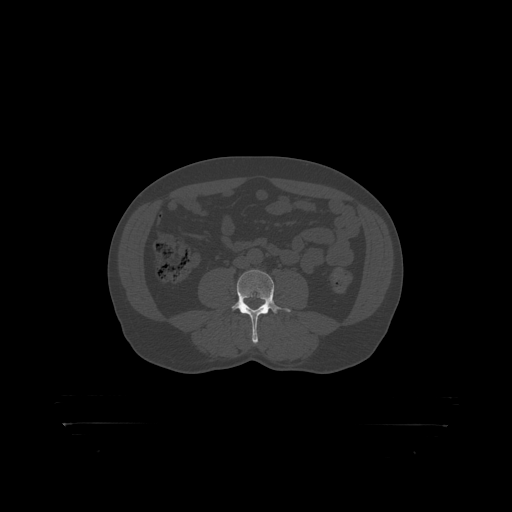
CT including the spine, one axial slice; slice 237 of 399 in the series (ordered by position); reconstruction kernel STANDARD; 120 kVp; bone window (W 1800 / L 400 HU); 1.25 mm slice thickness; 512 × 512 image matrix, field of view 650 × 650 mm. Male patient, age 46 years. From the clinical record (not read from this slice): primary cancer: skin.
Structures marked on this image (semi-automatic segmentation, software-assisted and operator-edited):
- L4 vertebra: bounding box (x1, y1, x2, y2) in pixels: (232, 270, 289, 319)